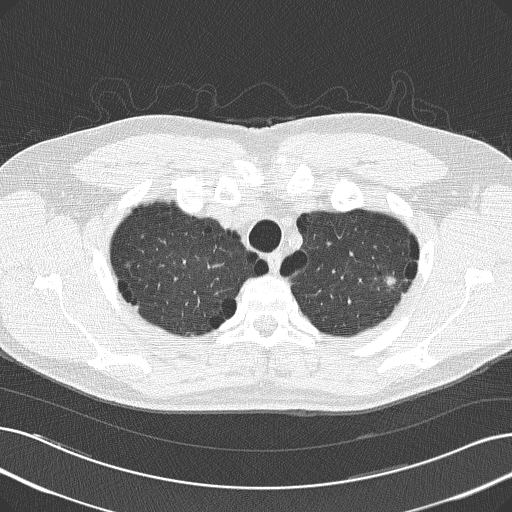
Low-dose screening chest CT, axial slice. Baseline annual screen. Lung window (W 1500 / L -600 HU). Slice 36 of 181 in the series. Male participant, aged 62 years at enrolment.
Lesion marked by an expert reader, bounding box [x1, y1, x2, y2] px = [368, 259, 419, 306]. The screening reader recorded 4 non-calcified nodules or masses ≥4 mm on this exam (left upper lobe, right upper lobe, right upper lobe, right middle lobe); which of them this box marks is not recorded. Later outcome: lung cancer diagnosed 383 days after this screen — adenocarcinoma, NOS, left upper lobe, well differentiated (G1), stage IB (AJCC 6th edition), 17 mm at pathology.